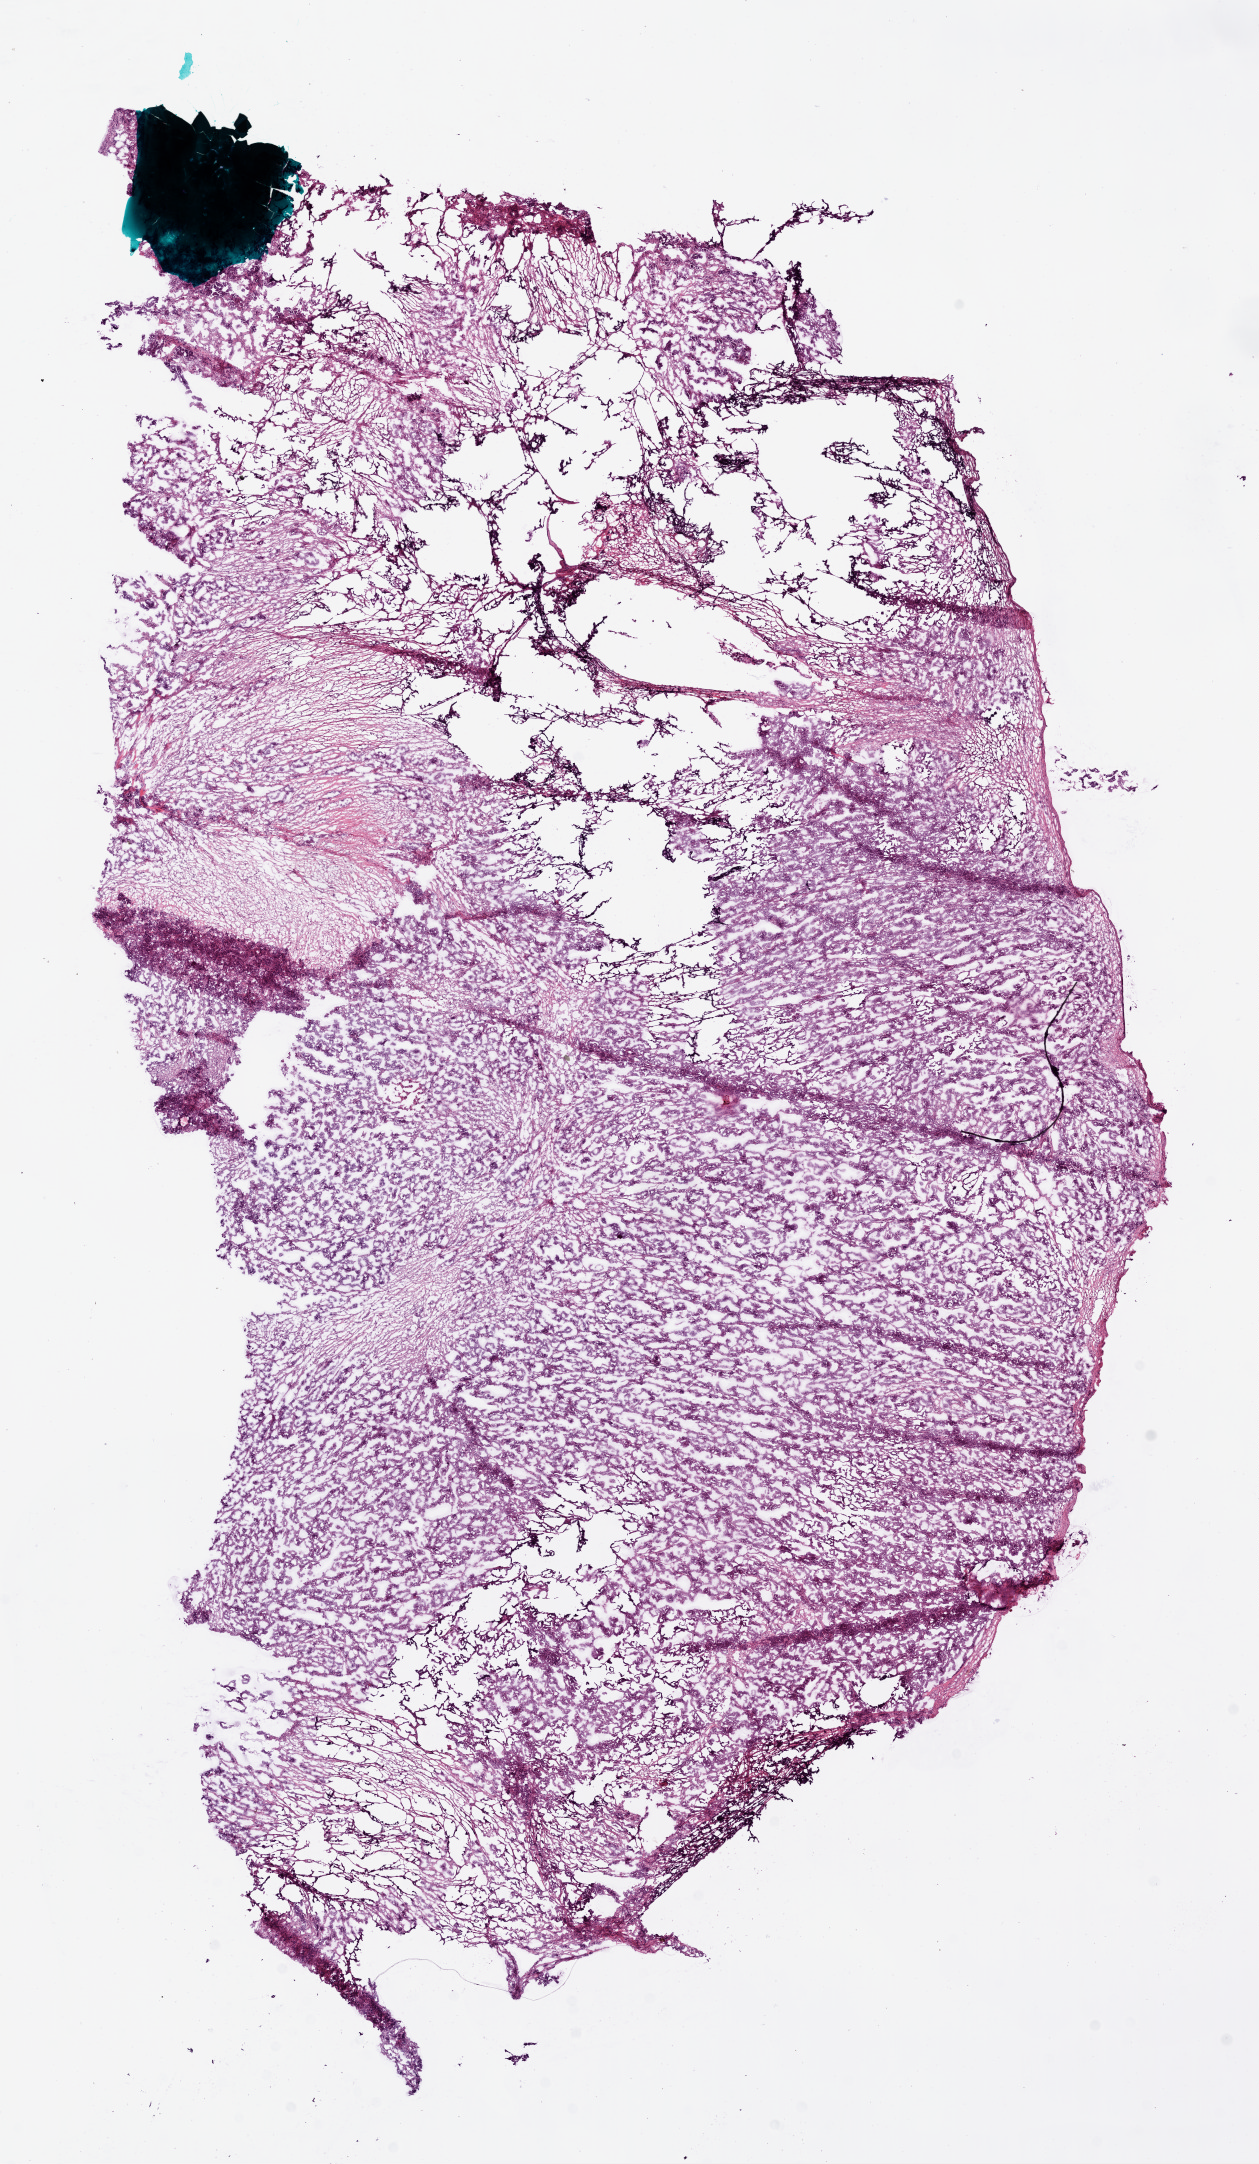
Hematoxylin and eosin (H&E) stained whole-slide image, a low-resolution overview of the entire scanned area, about 10.2 x 17.5 mm (from a 20x scan), frozen section from the bottom of the tissue portion, sample: primary tumour, ovary. Female patient; age at initial diagnosis 63 years. Histologic grade: G3 (poorly differentiated). Composition of this section per pathologist review: tumour nuclei 95%, normal cells 0%, stromal cells 0%, necrosis 5%.
Diagnosis: Serous cystadenocarcinoma, NOS. Laterality: bilateral. FIGO stage: IIIC.